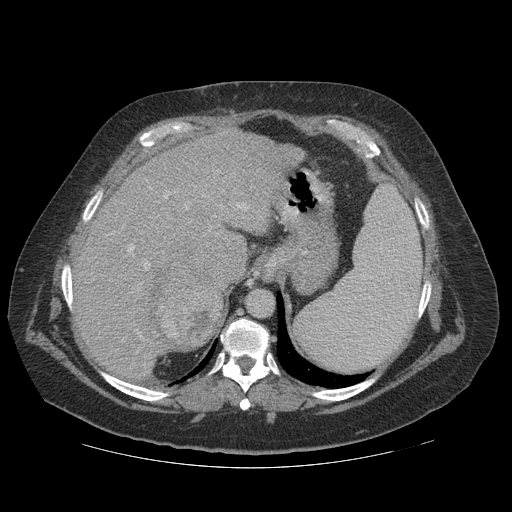
Contrast-enhanced abdominal CT (liver protocol), one axial slice; position 87 of 121 along the scan axis; 140 kVp; soft-tissue window (W 400 / L 40 HU); 512 × 512 image matrix. Case-level facts recorded for this patient, not image findings: diagnosis: hepatocellular carcinoma (patient treated with transarterial chemoembolisation; whether this scan precedes or follows treatment is not stated here); TNM stage (as recorded): Stage-IIIA; Child-Pugh class: A; tumour differentiation: well differentiated; tumour nodularity: multinodular.
Structures marked on this image (semi-automatically segmented with operator editing):
- liver parenchyma outside the tumour (the mass and vessels are separate outlines, so this box may not span the whole liver): bounding box <72,128,306,376> (left, top, right, bottom; pixels)
- mass: <129,262,222,355>
- liver vessels: <106,170,250,365>